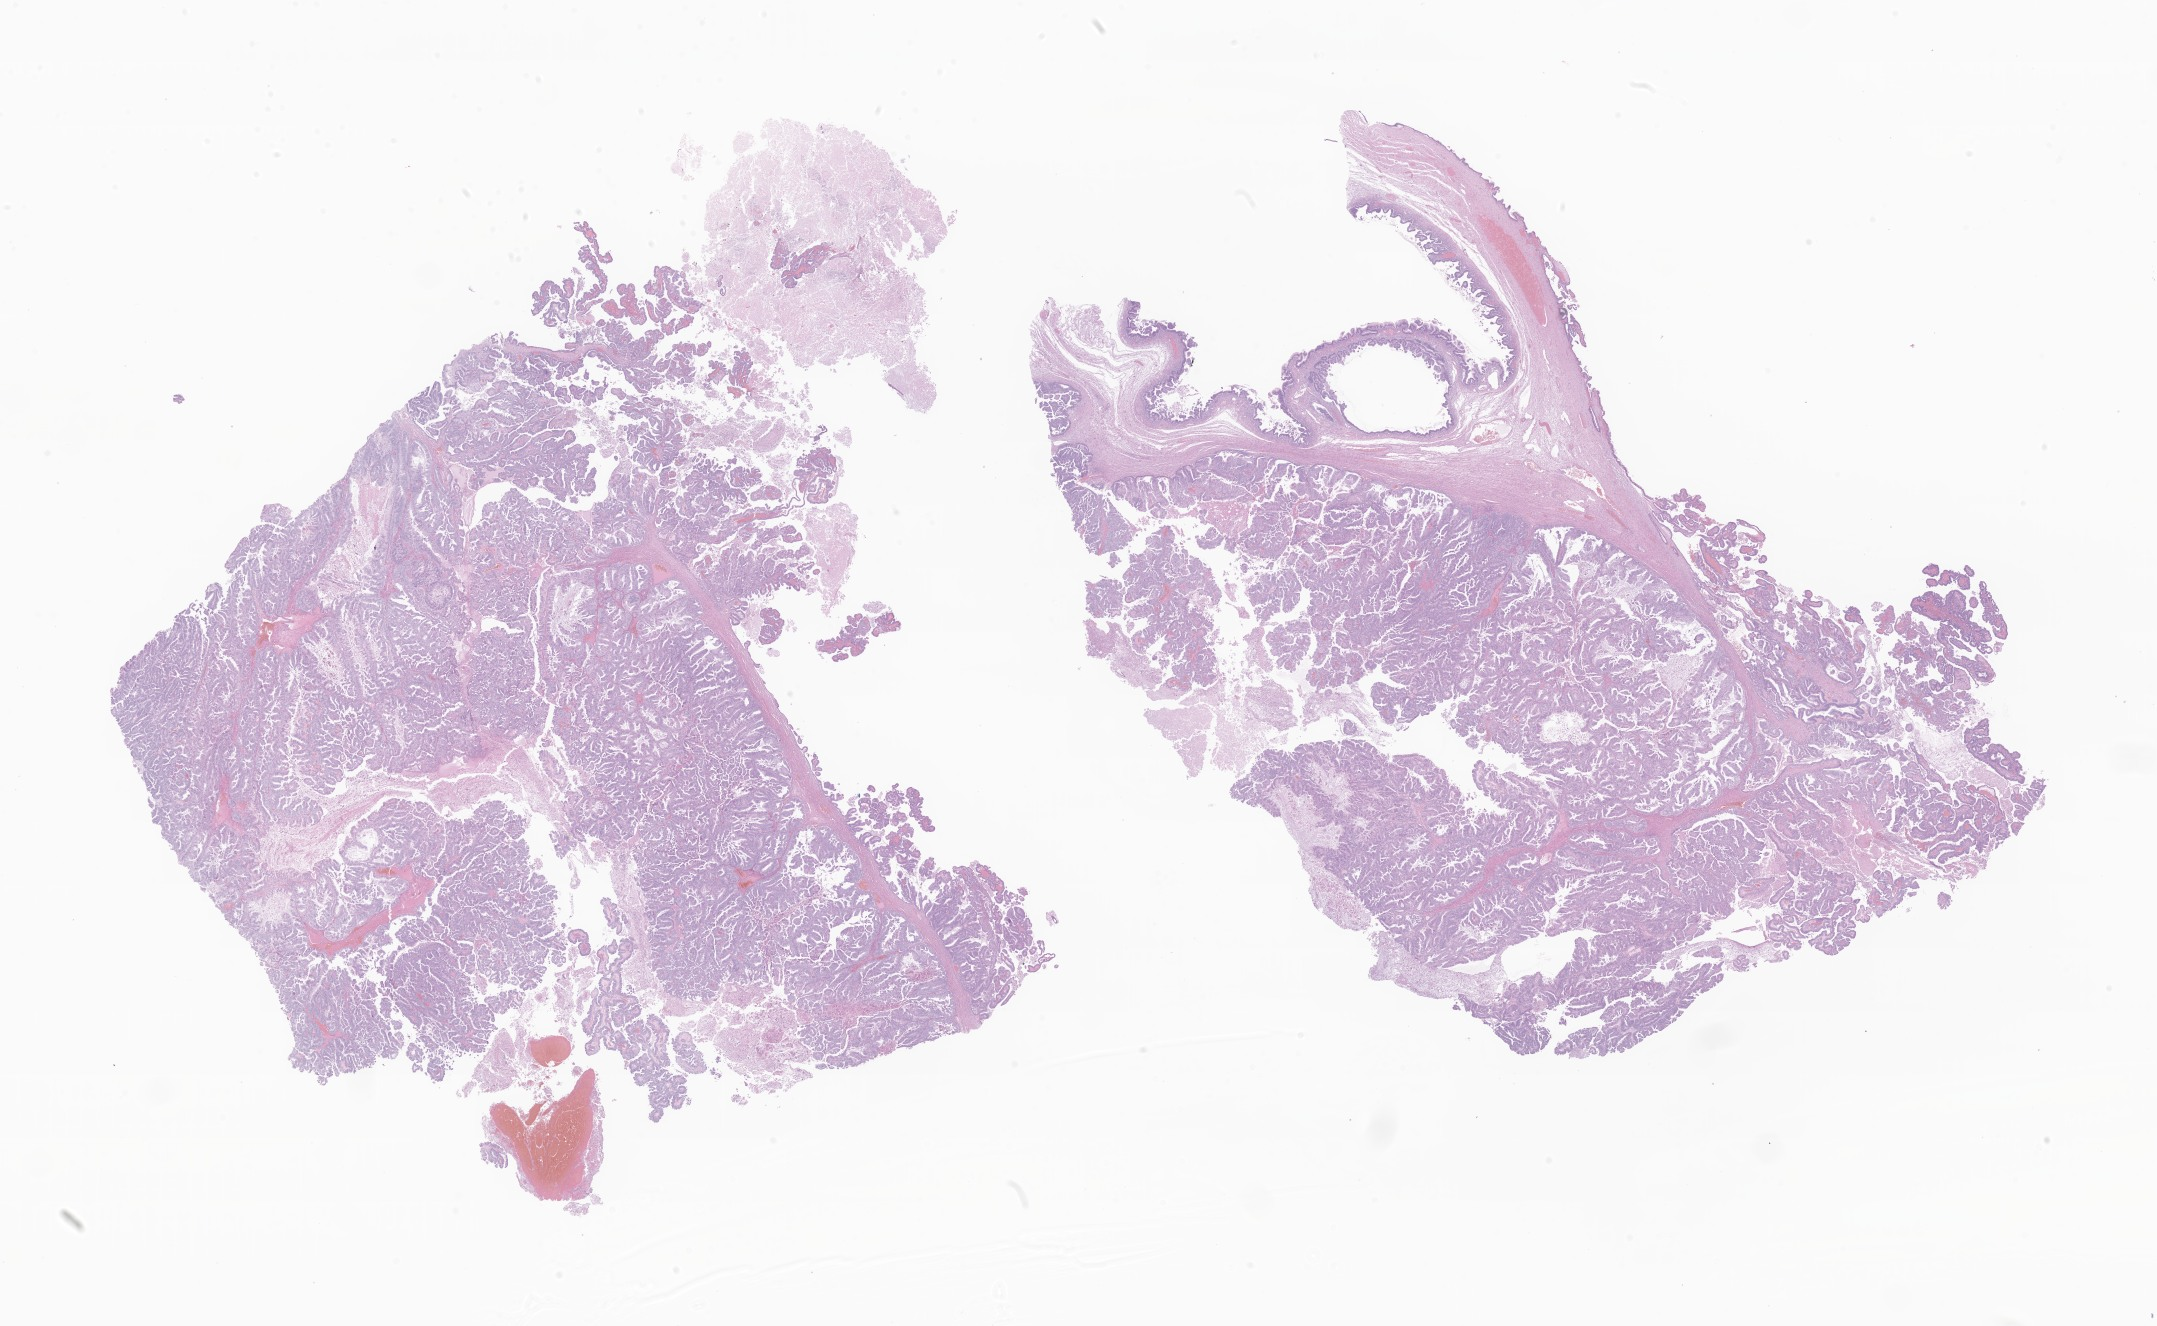
Digitized haematoxylin and eosin-stained section of tumor tissue from the ovary, shown as a low-resolution overview of the whole scanned area (about 36.4 x 22.4 mm). FFPE section. Female patient, age 190 months (15 years 10 months).
* diagnosis (ICD-O-3 morphology term): Mucinous cystadenocarcinoma, NOS